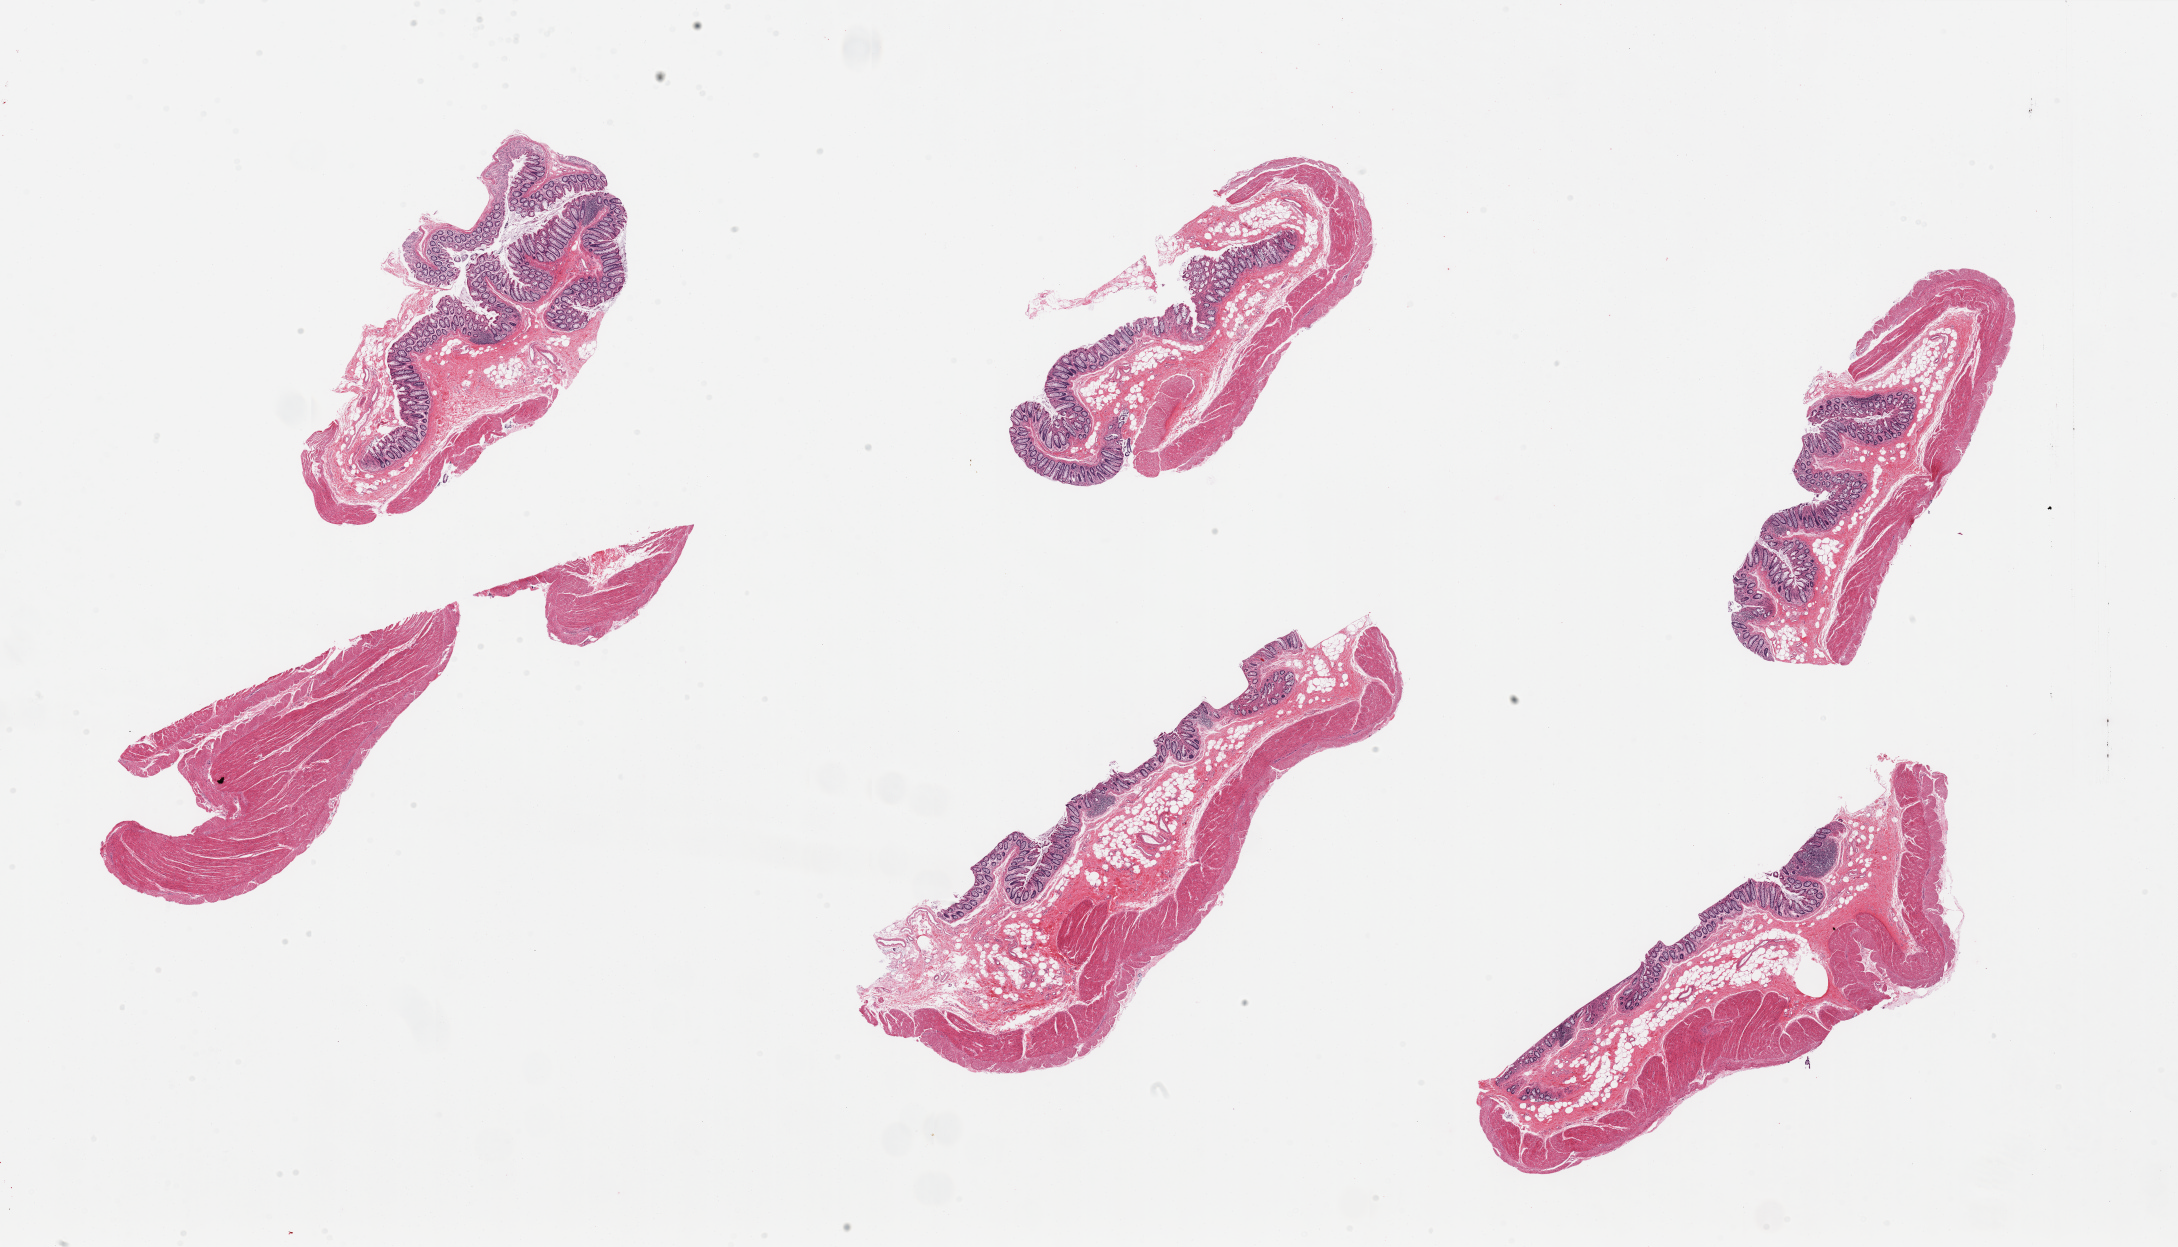
Whole-slide image, haematoxylin and eosin stain — low-resolution overview of the scanned area, about 34.5 x 19.7 mm (acquisition: 20x scan). PAXgene-fixed paraffin-embedded (PFPE) section. Target tissue: transverse colon. Tissue donor sample. Donor: male.
- pathologist's review note for this sample: 6 pieces, mucosa reasonably well preserved, focally approaches score '2' in a few foci; ~10% total thicknees, averaging 0.3-0.4mm